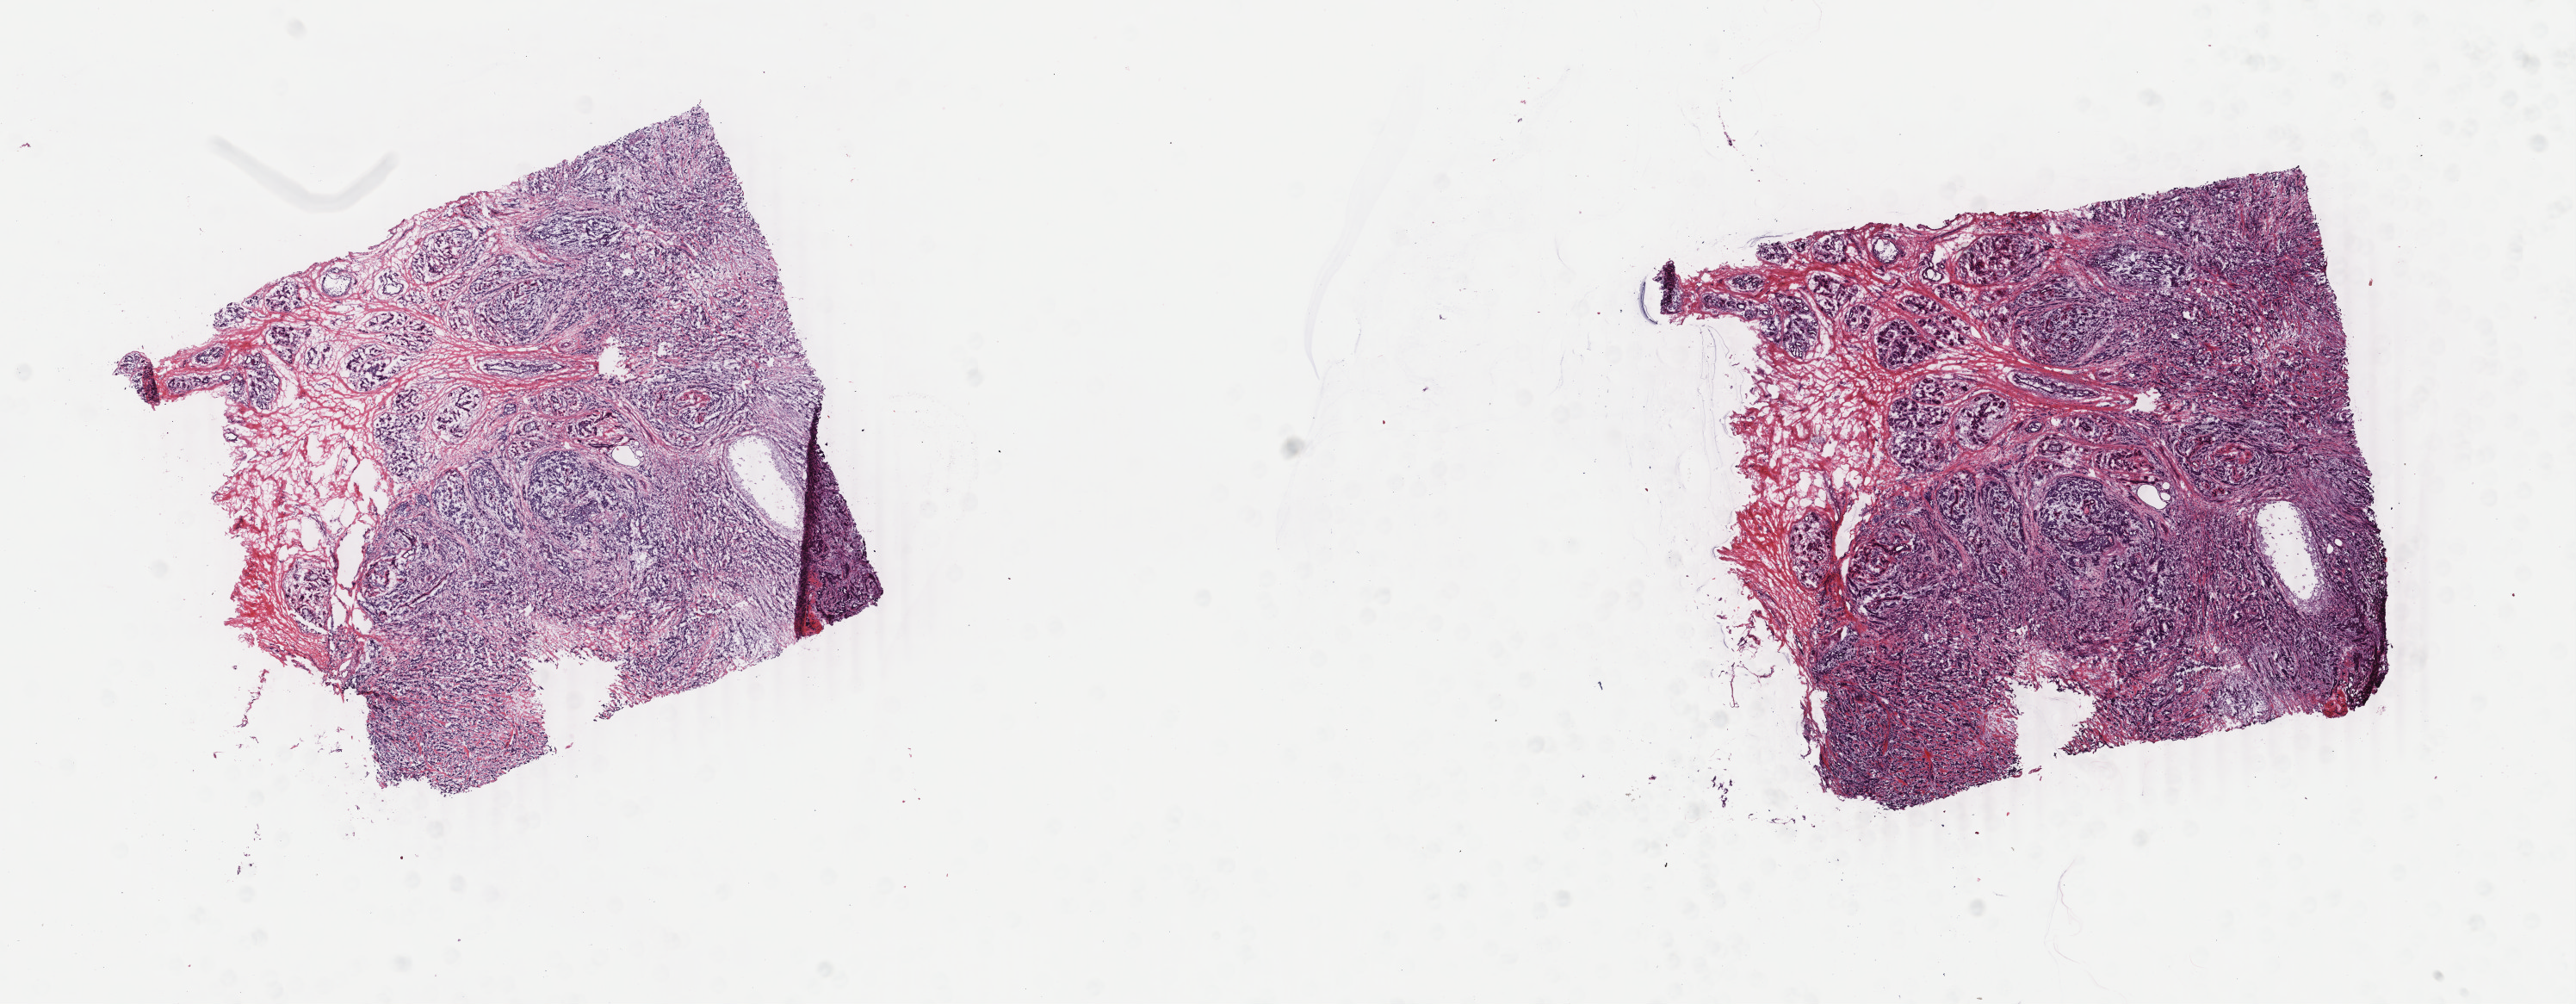
Whole-slide histology image, Hematoxylin and eosin (H&E) stained, a low-resolution overview of the entire scanned area, about 23.8 x 9.3 mm; frozen section; primary tumour sample from the breast. Female, age 51 years at initial diagnosis. Pathologist review of this section (percent, as recorded): tumour cells 80%, tumour nuclei 80%, normal cells 0%, stromal cells 15%, necrosis 5%. Infiltration values recorded for this section: lymphocyte infiltration 30%, monocyte infiltration 10%, neutrophil infiltration 20%.
* AJCC pathologic stage: IIA
* lymph nodes positive (case pathology): 0 of 2 examined
* diagnosis: Infiltrating duct carcinoma, NOS